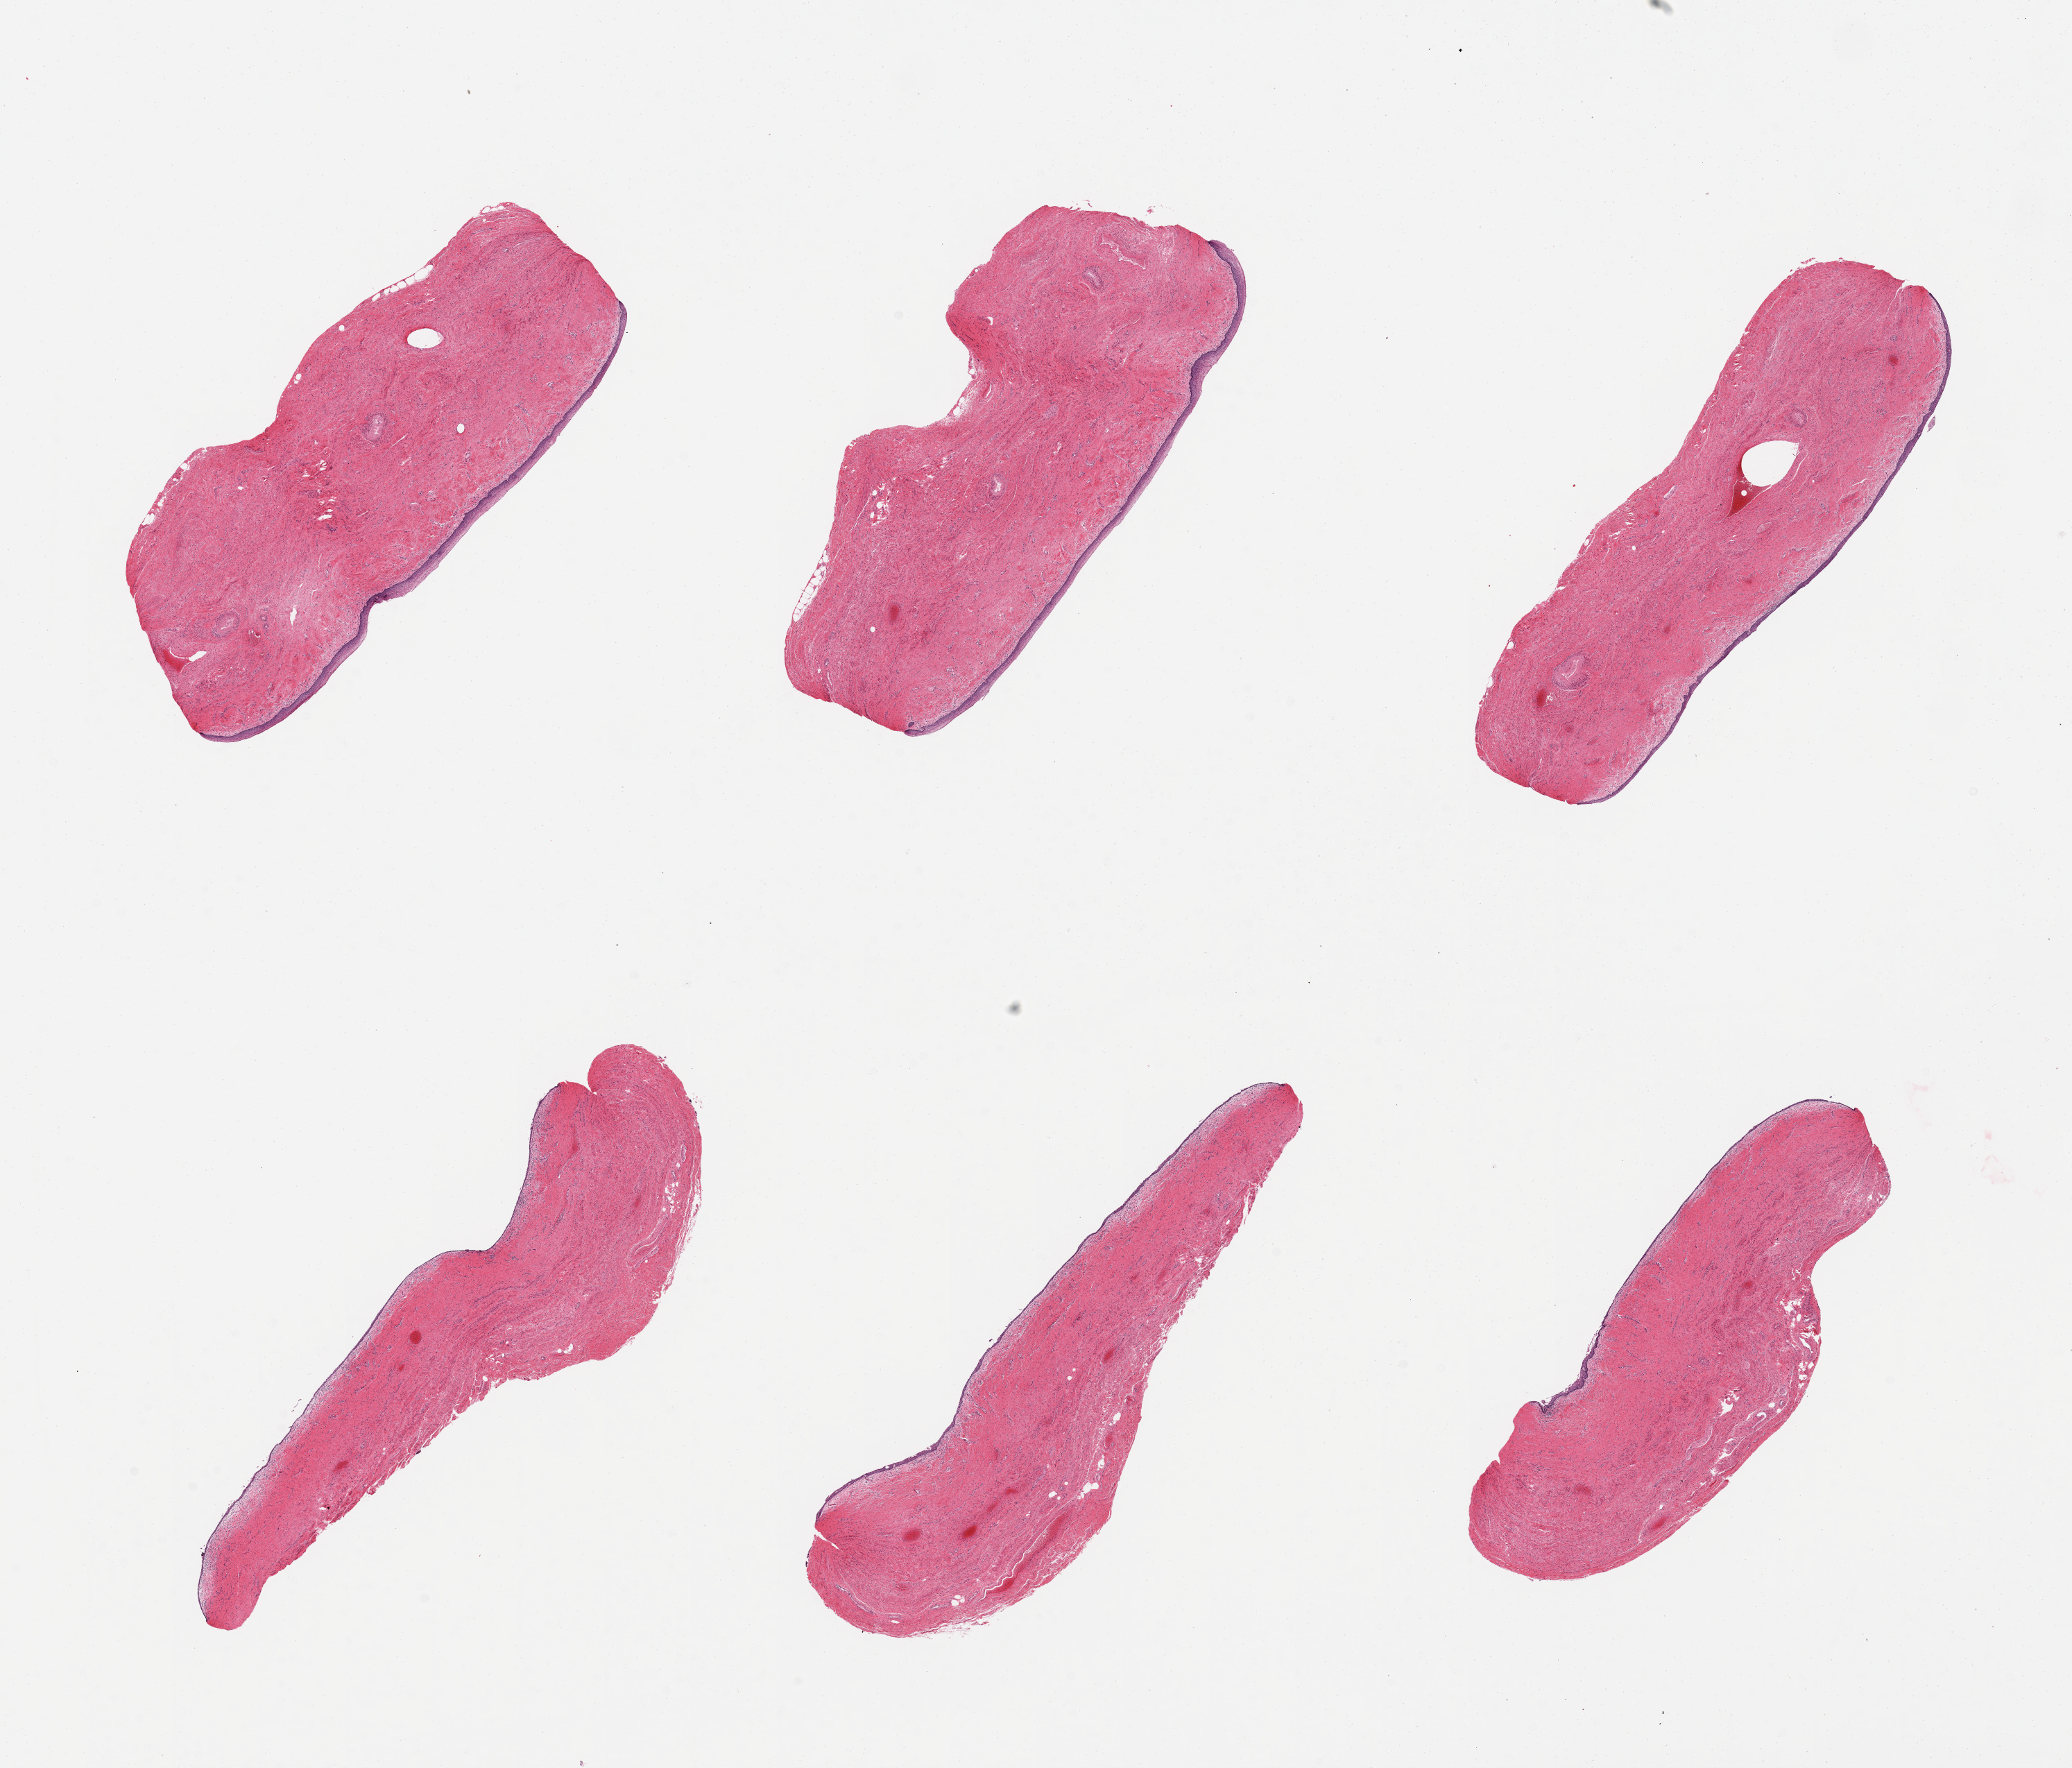
Digitized haematoxylin and eosin-stained section, low-resolution overview of the scanned area, about 23.6 x 20.2 mm. PAXgene-fixed paraffin-embedded (PFPE) section. Target tissue: vagina. Tissue donor sample. Female donor.
* reviewer comment on this tissue sample: 6 pieces; squamous mucosa is 1-3% thickness